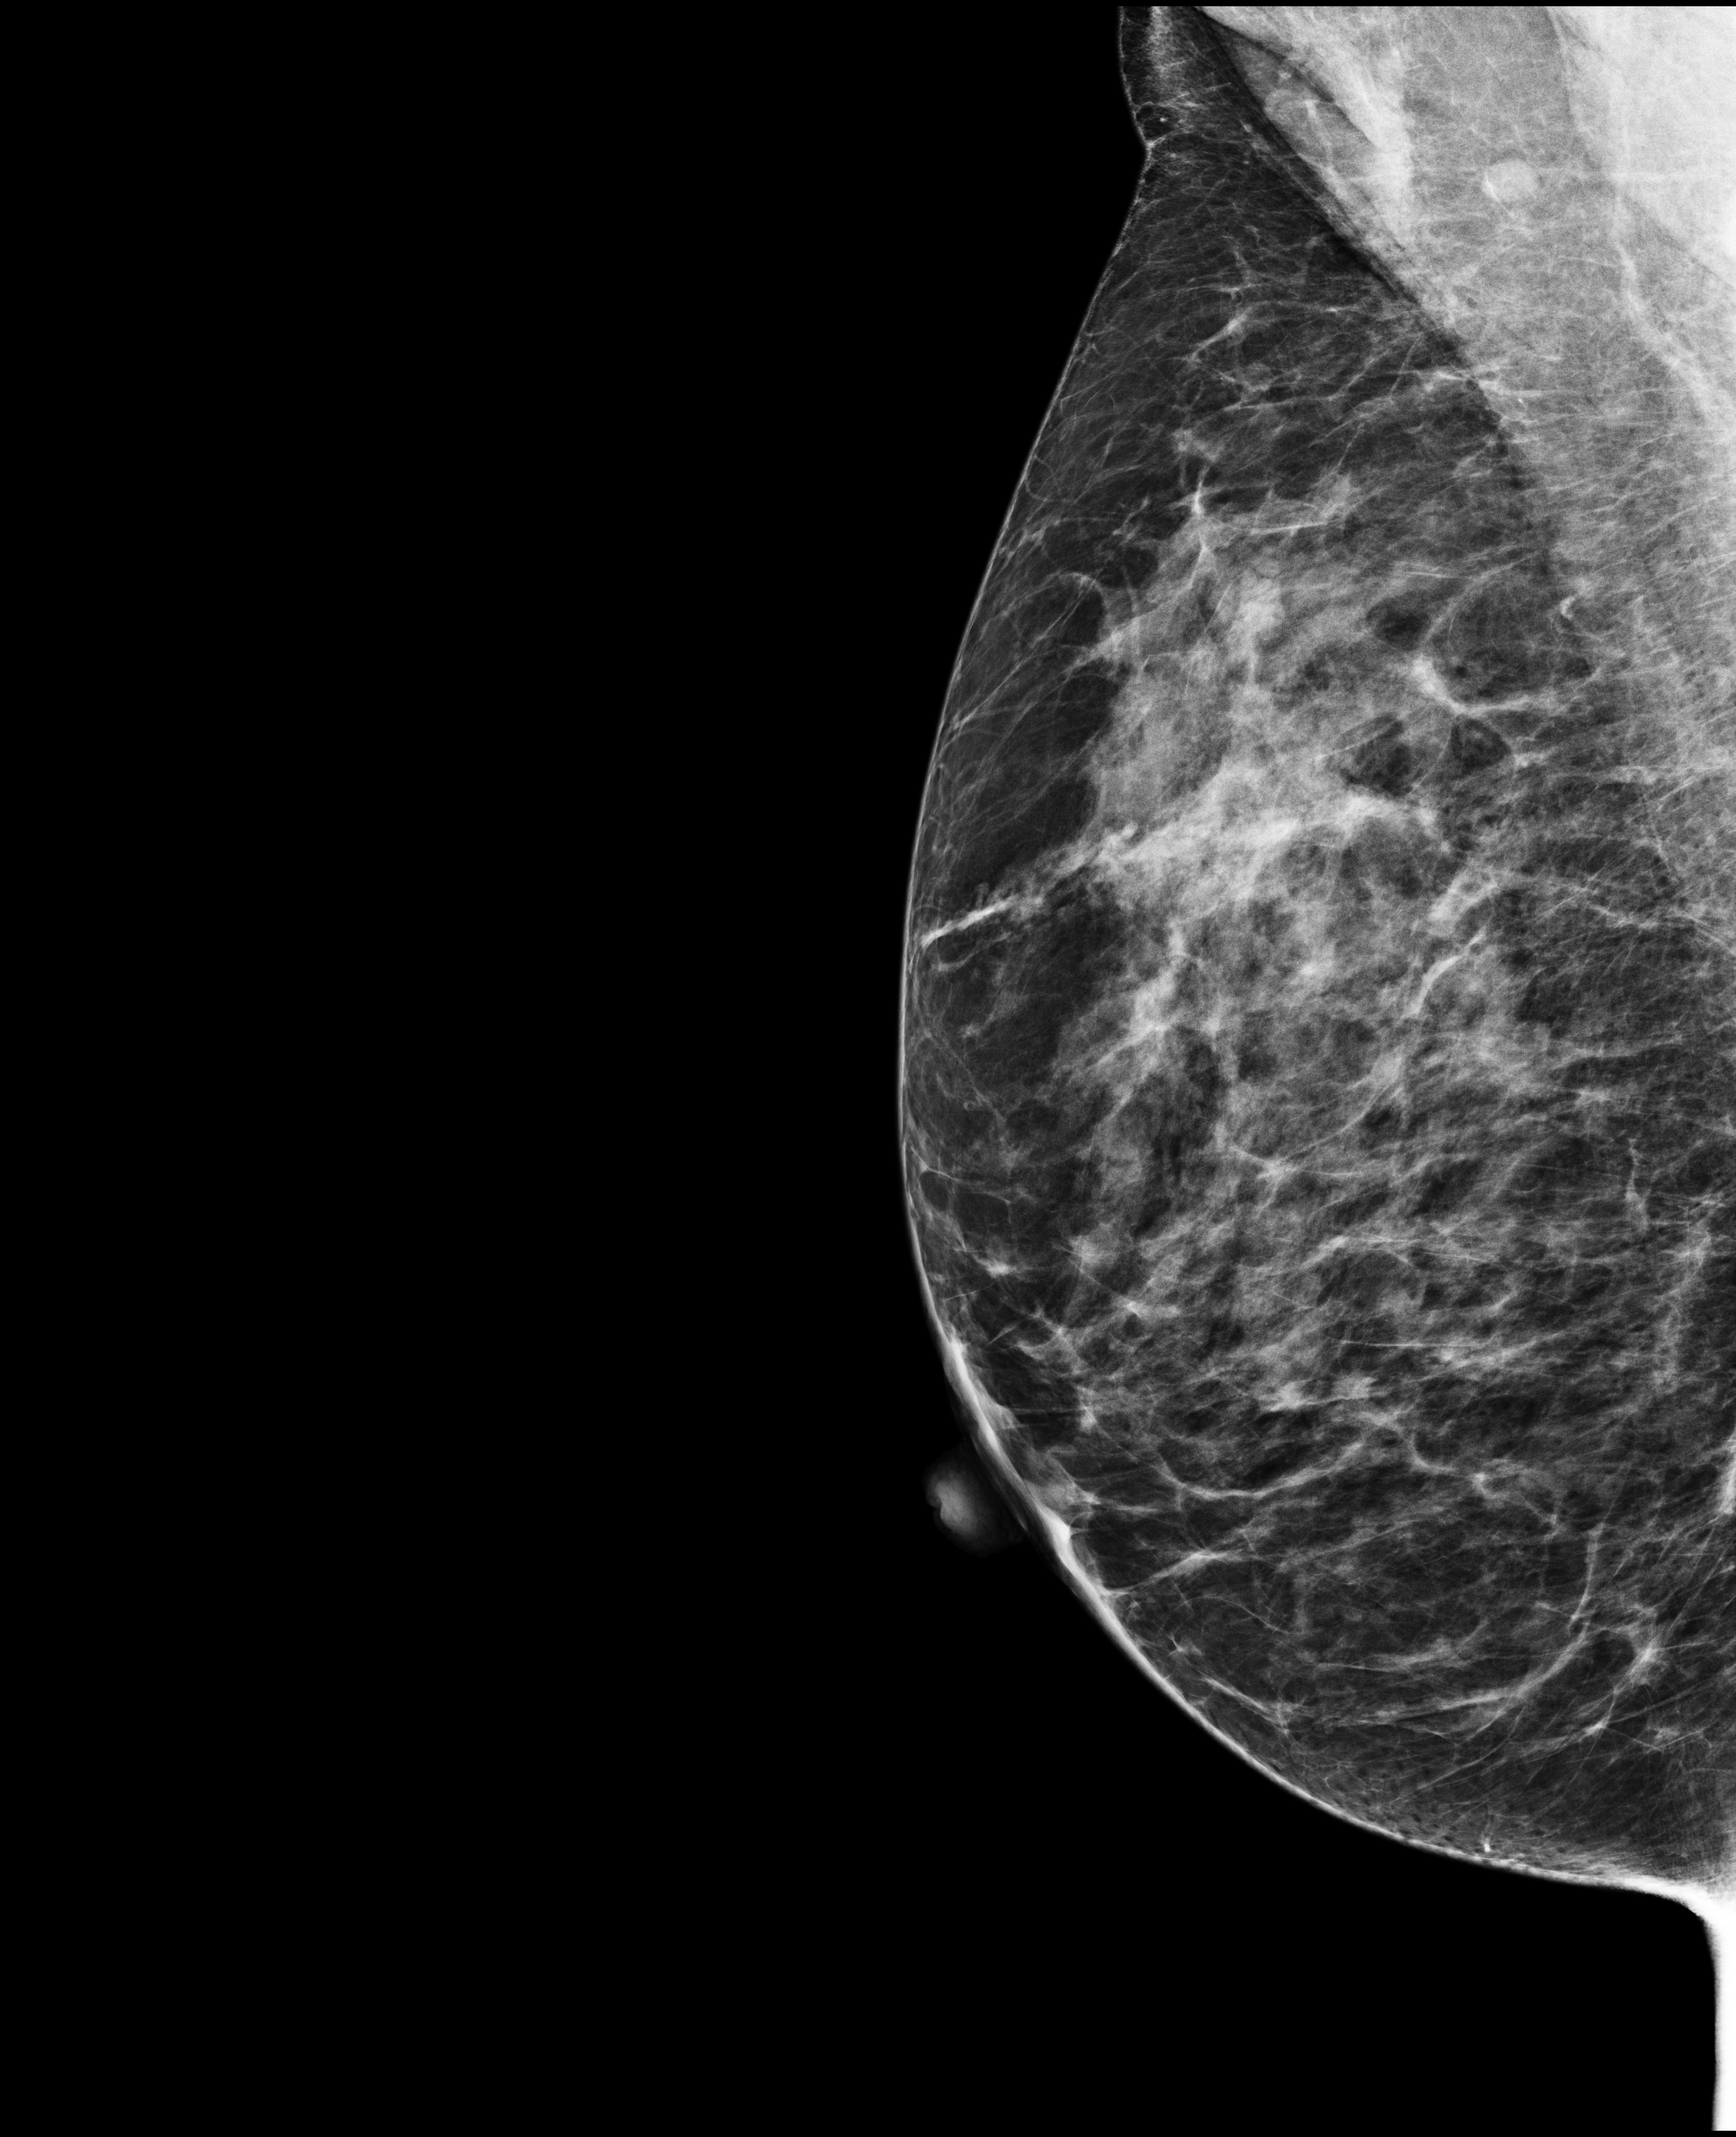
Annual screening mammography examination, compressed breast thickness 52 mm, system: Selenia Dimensions. Patient aged 45 years (female).
Image type: full-field digital mammogram. Breast: right. Projection: MLO view. Breast density at the screening exam (both breasts): heterogeneously dense (BI-RADS density category c). Final BI-RADS assessment for this screening round (tomosynthesis exam, both breasts): category 1. Recall: no recall after this screen.